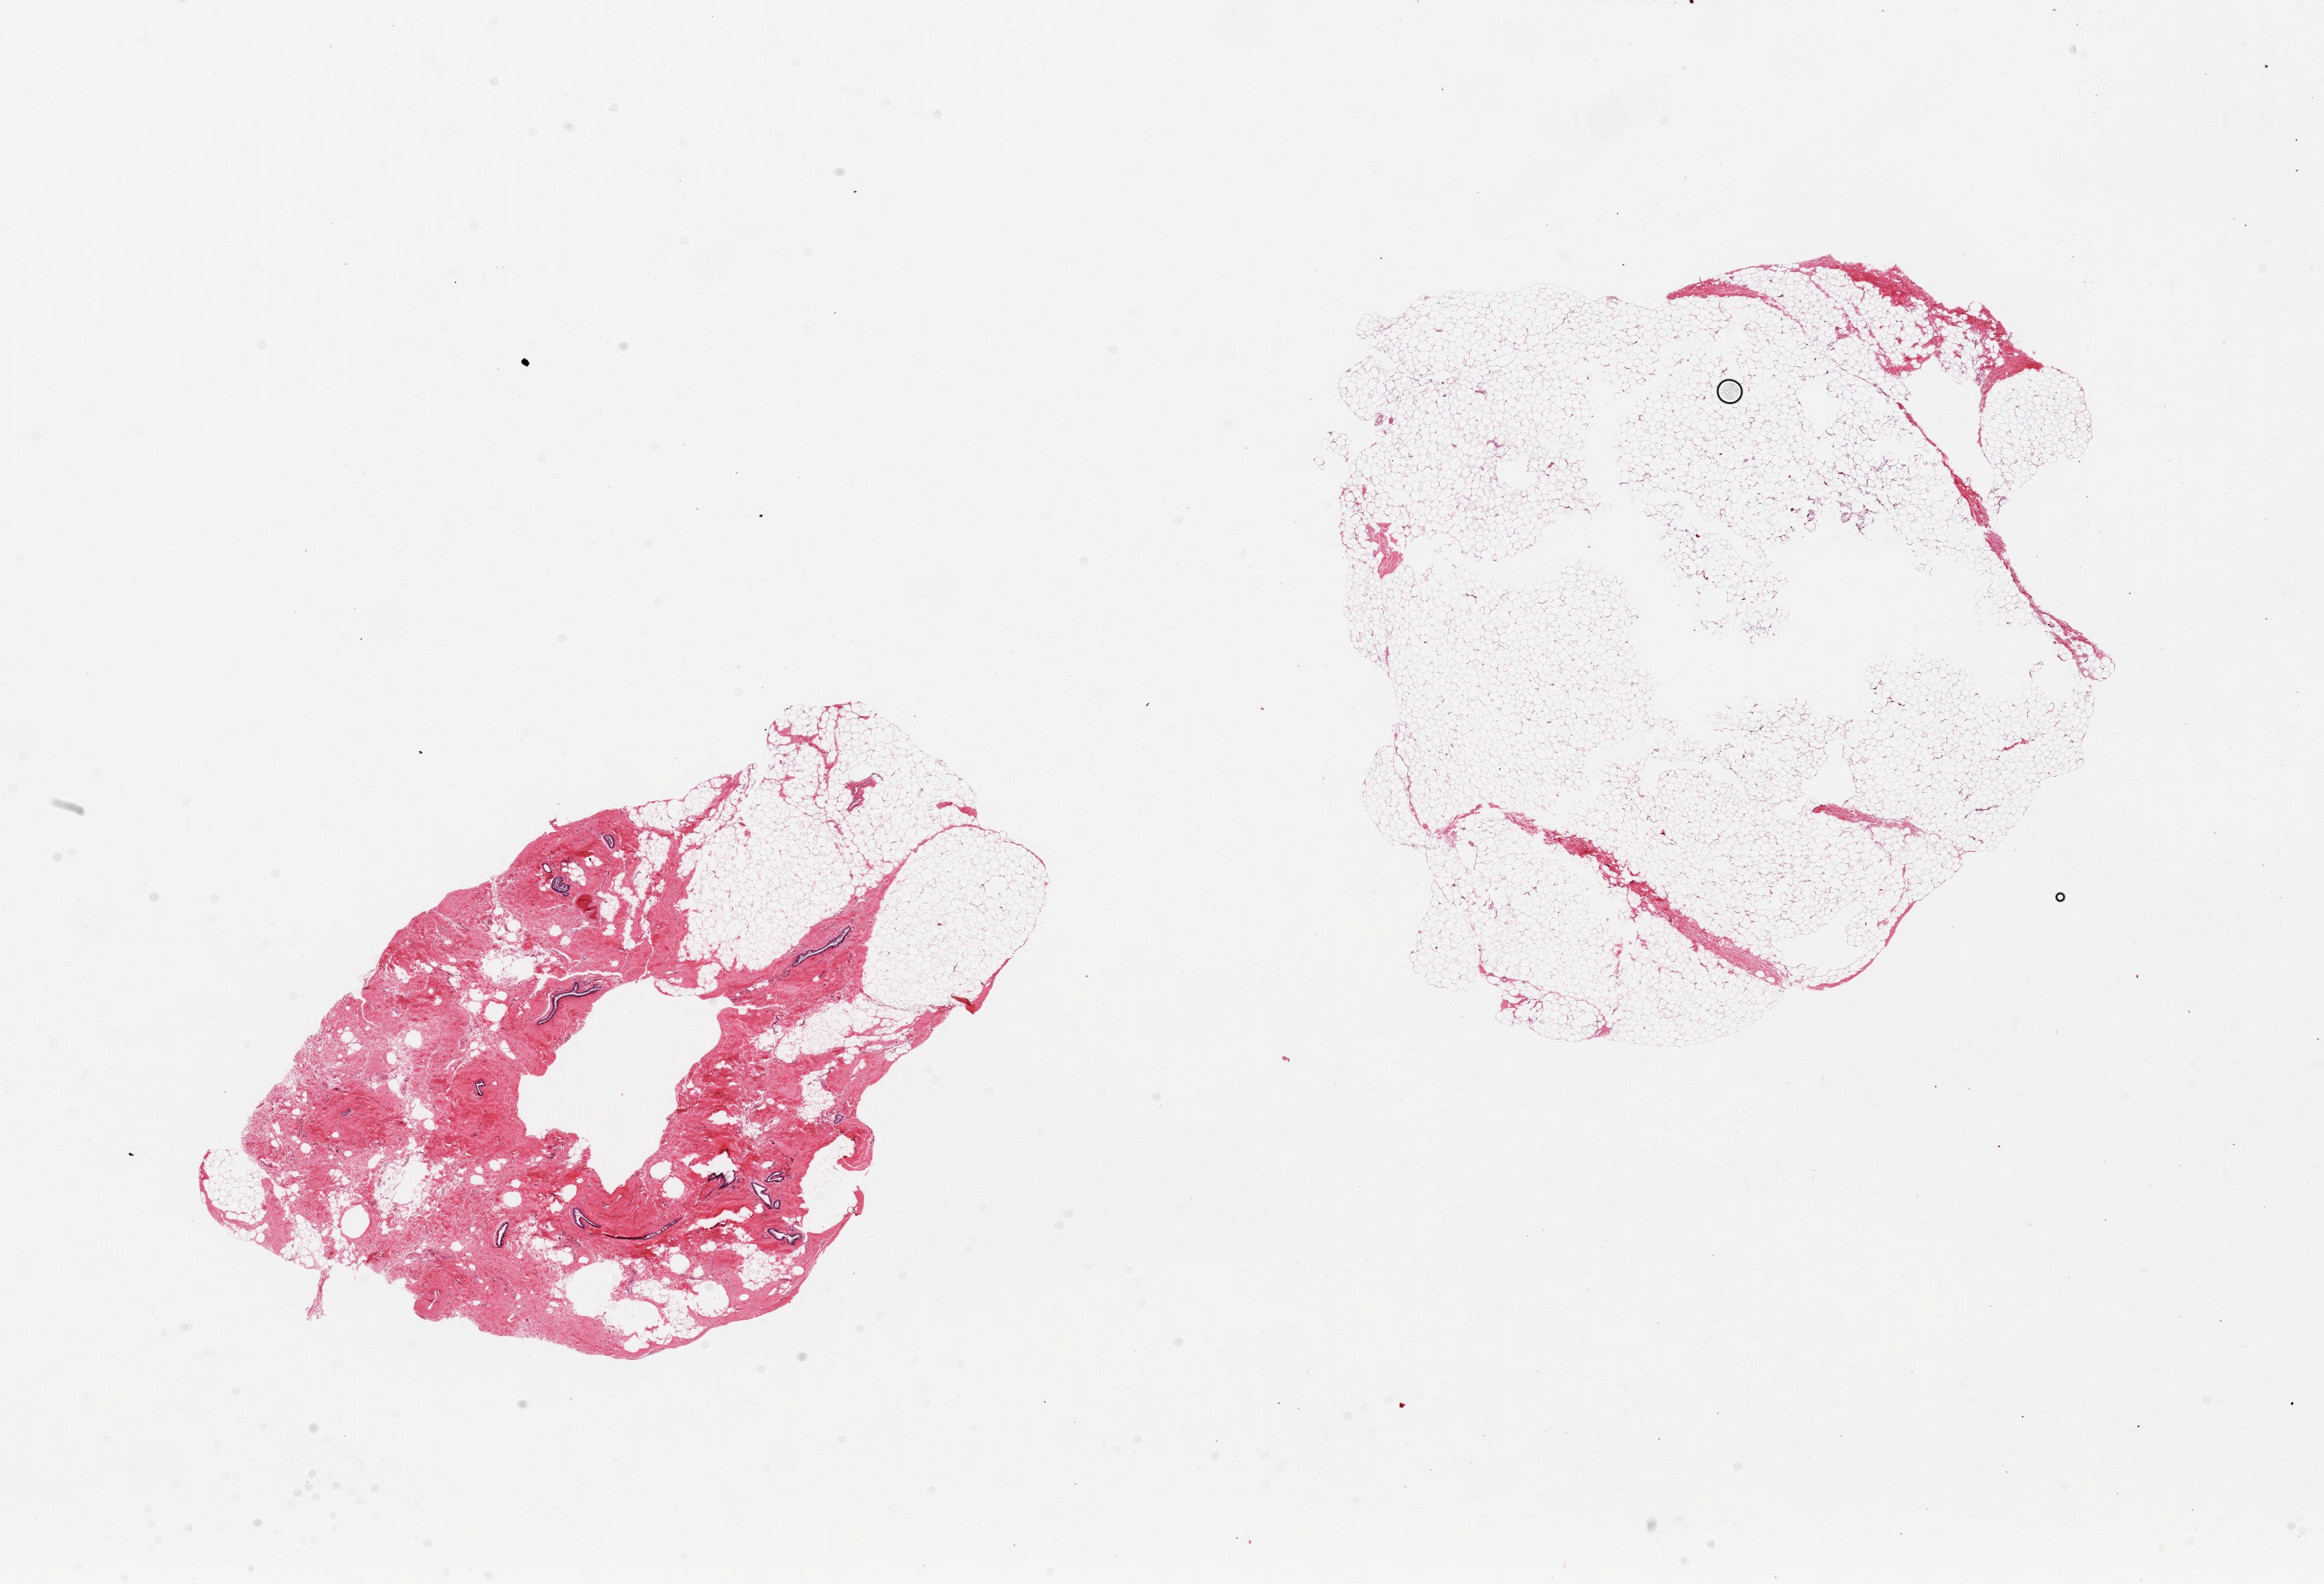
Digitized hematoxylin and eosin (H&E)-stained section, whole scanned area (about 27.6 x 18.8 mm) shown as a low-resolution overview, PAXgene-fixed, paraffin-embedded tissue, section of breast (target tissue), donor tissue sample. Donor: male.
Pathologist's review note for this sample: 2 pieces, one section with gynecomastoid stromal hyperplasia and visible ductal elements; Other section is fat/fibrous tissue.